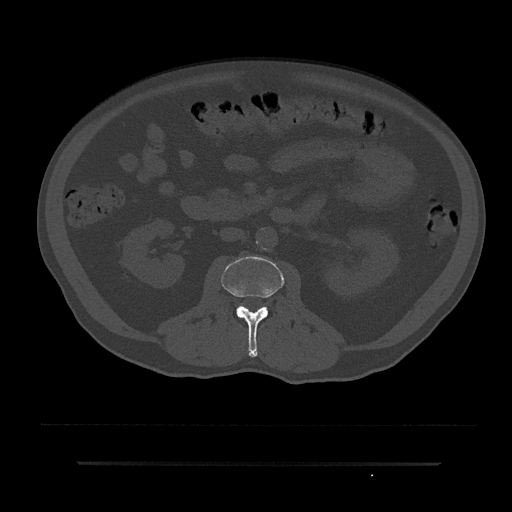
CT including the spine, one axial slice. Position 58 of 797 along the scan axis. Bone window (W 1800 / L 400 HU). 0.5 mm slice thickness. 512 × 512 image matrix, field of view 464 × 464 mm. Patient: male, 59 years. From the clinical record (not read from this slice): primary cancer: bile ducts.
Annotated regions visible in this slice (semi-automatically segmented with operator editing):
- L2 vertebra: bounding box (x1, y1, x2, y2) in pixels: (221, 256, 284, 357)